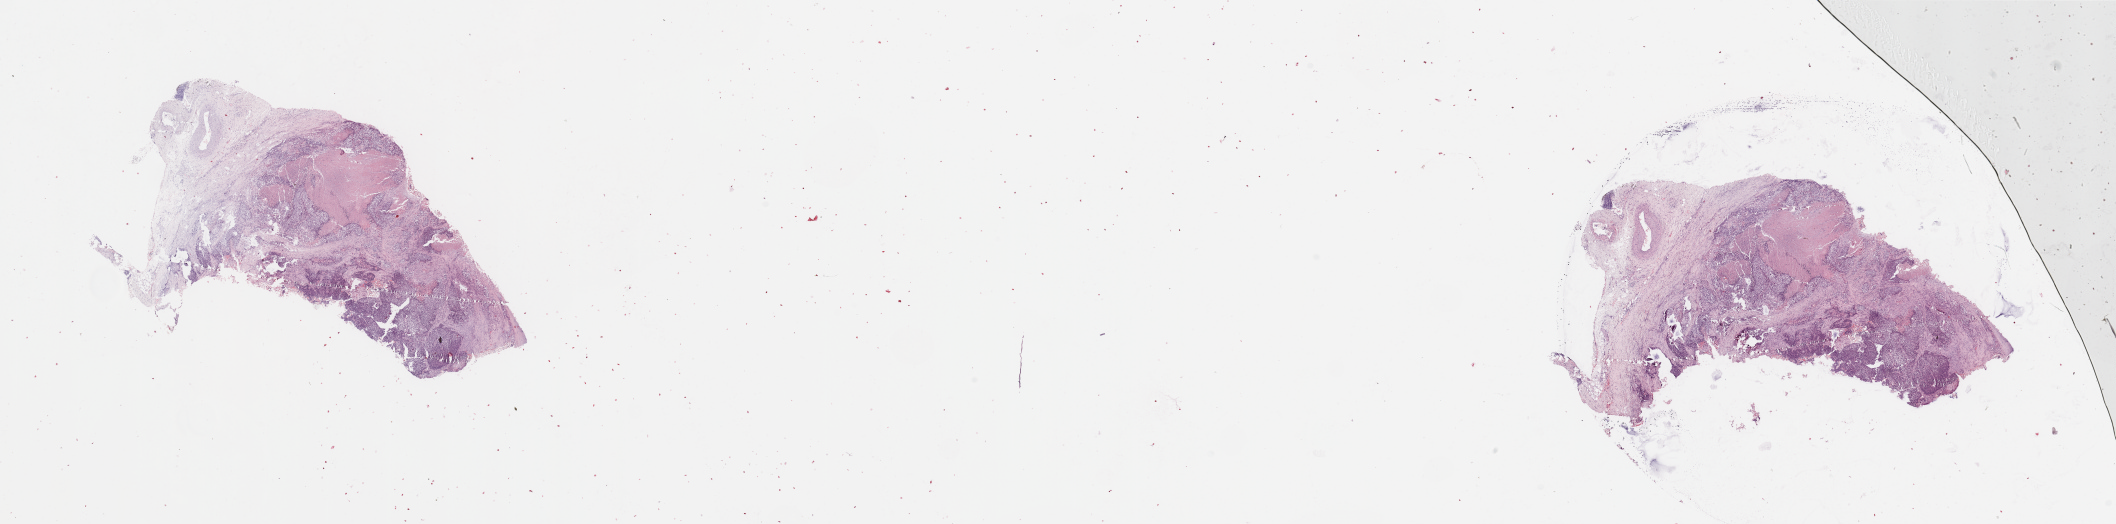
Digitized H&E tissue section (whole slide), whole scanned area (about 33.5 x 8.3 mm) shown as a low-resolution overview; lung, tumour tissue. 65-year-old male patient. Histologic grade: G3 (poorly differentiated).
AJCC pathologic stage: IB. Histologic diagnosis: Squamous cell carcinoma, NOS.